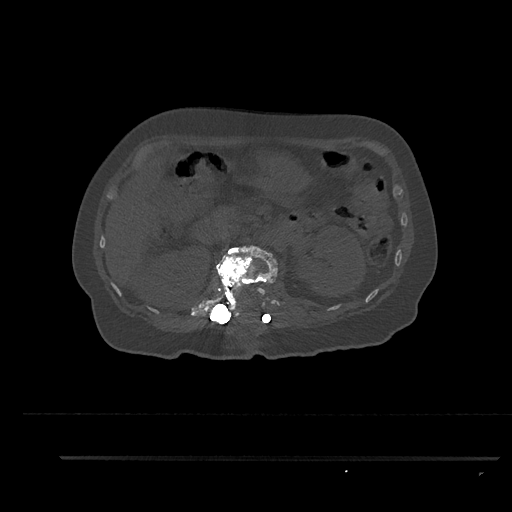
CT including the spine, one axial slice. Slice 210 of 797 in the series (ordered by position). 120 kVp. Bone window (W 1800 / L 400 HU). 0.5 mm slice thickness. 512 × 512 image matrix, field of view 408 × 408 mm. Female patient, age 44 years. From the clinical record (not read from this slice): primary cancer: renal; vertebrae with lytic lesions (as recorded): L1.
Outlined on this slice (semi-automatically segmented with operator editing):
- L1 vertebra: box from (x=204, y=245) to (x=278, y=323) px